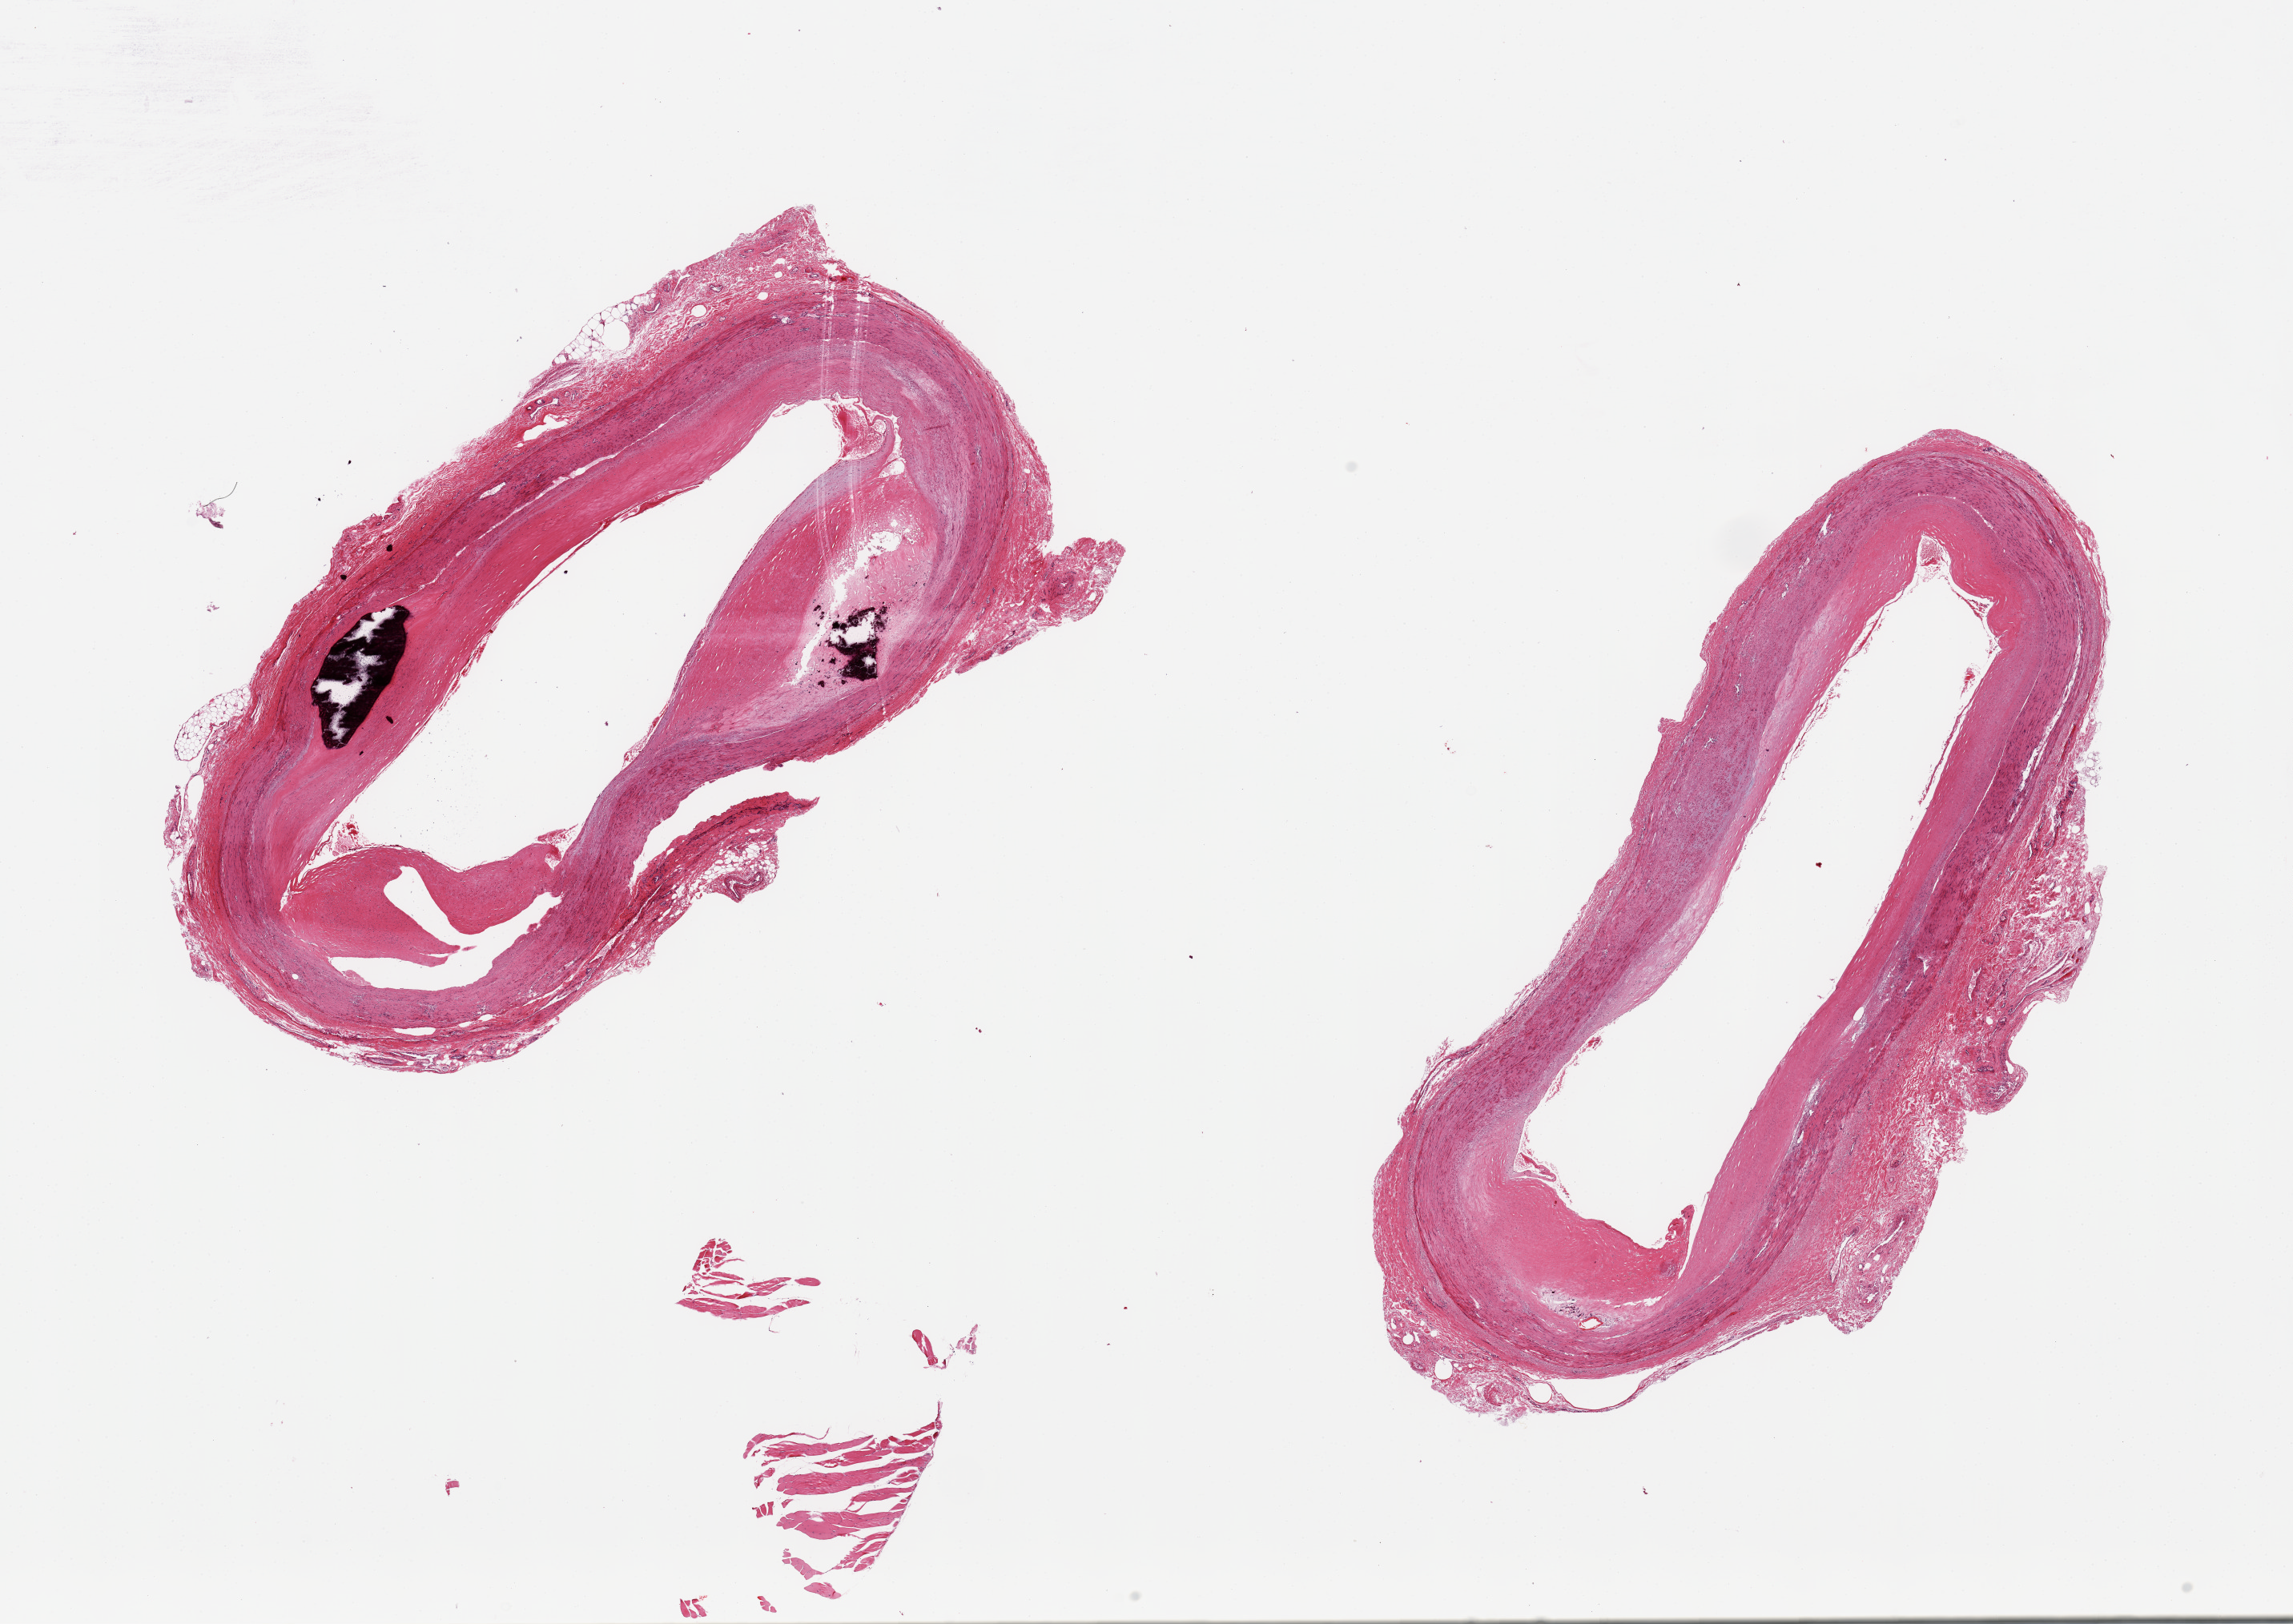
Digitized haematoxylin and eosin-stained section, brightfield — shown as a low-resolution overview of the whole scanned area (about 22.6 x 16.0 mm), PAXgene-fixed, paraffin-embedded tissue, section of tibial artery (target tissue), donor tissue sample. Donor sex: male.
* pathologist's review note for this sample: 2 pieces; 1 with moderate plaque & 2 calcific deposits up to 1.5mm; other with mild plaque; well trimmed adventitia up to 1mm